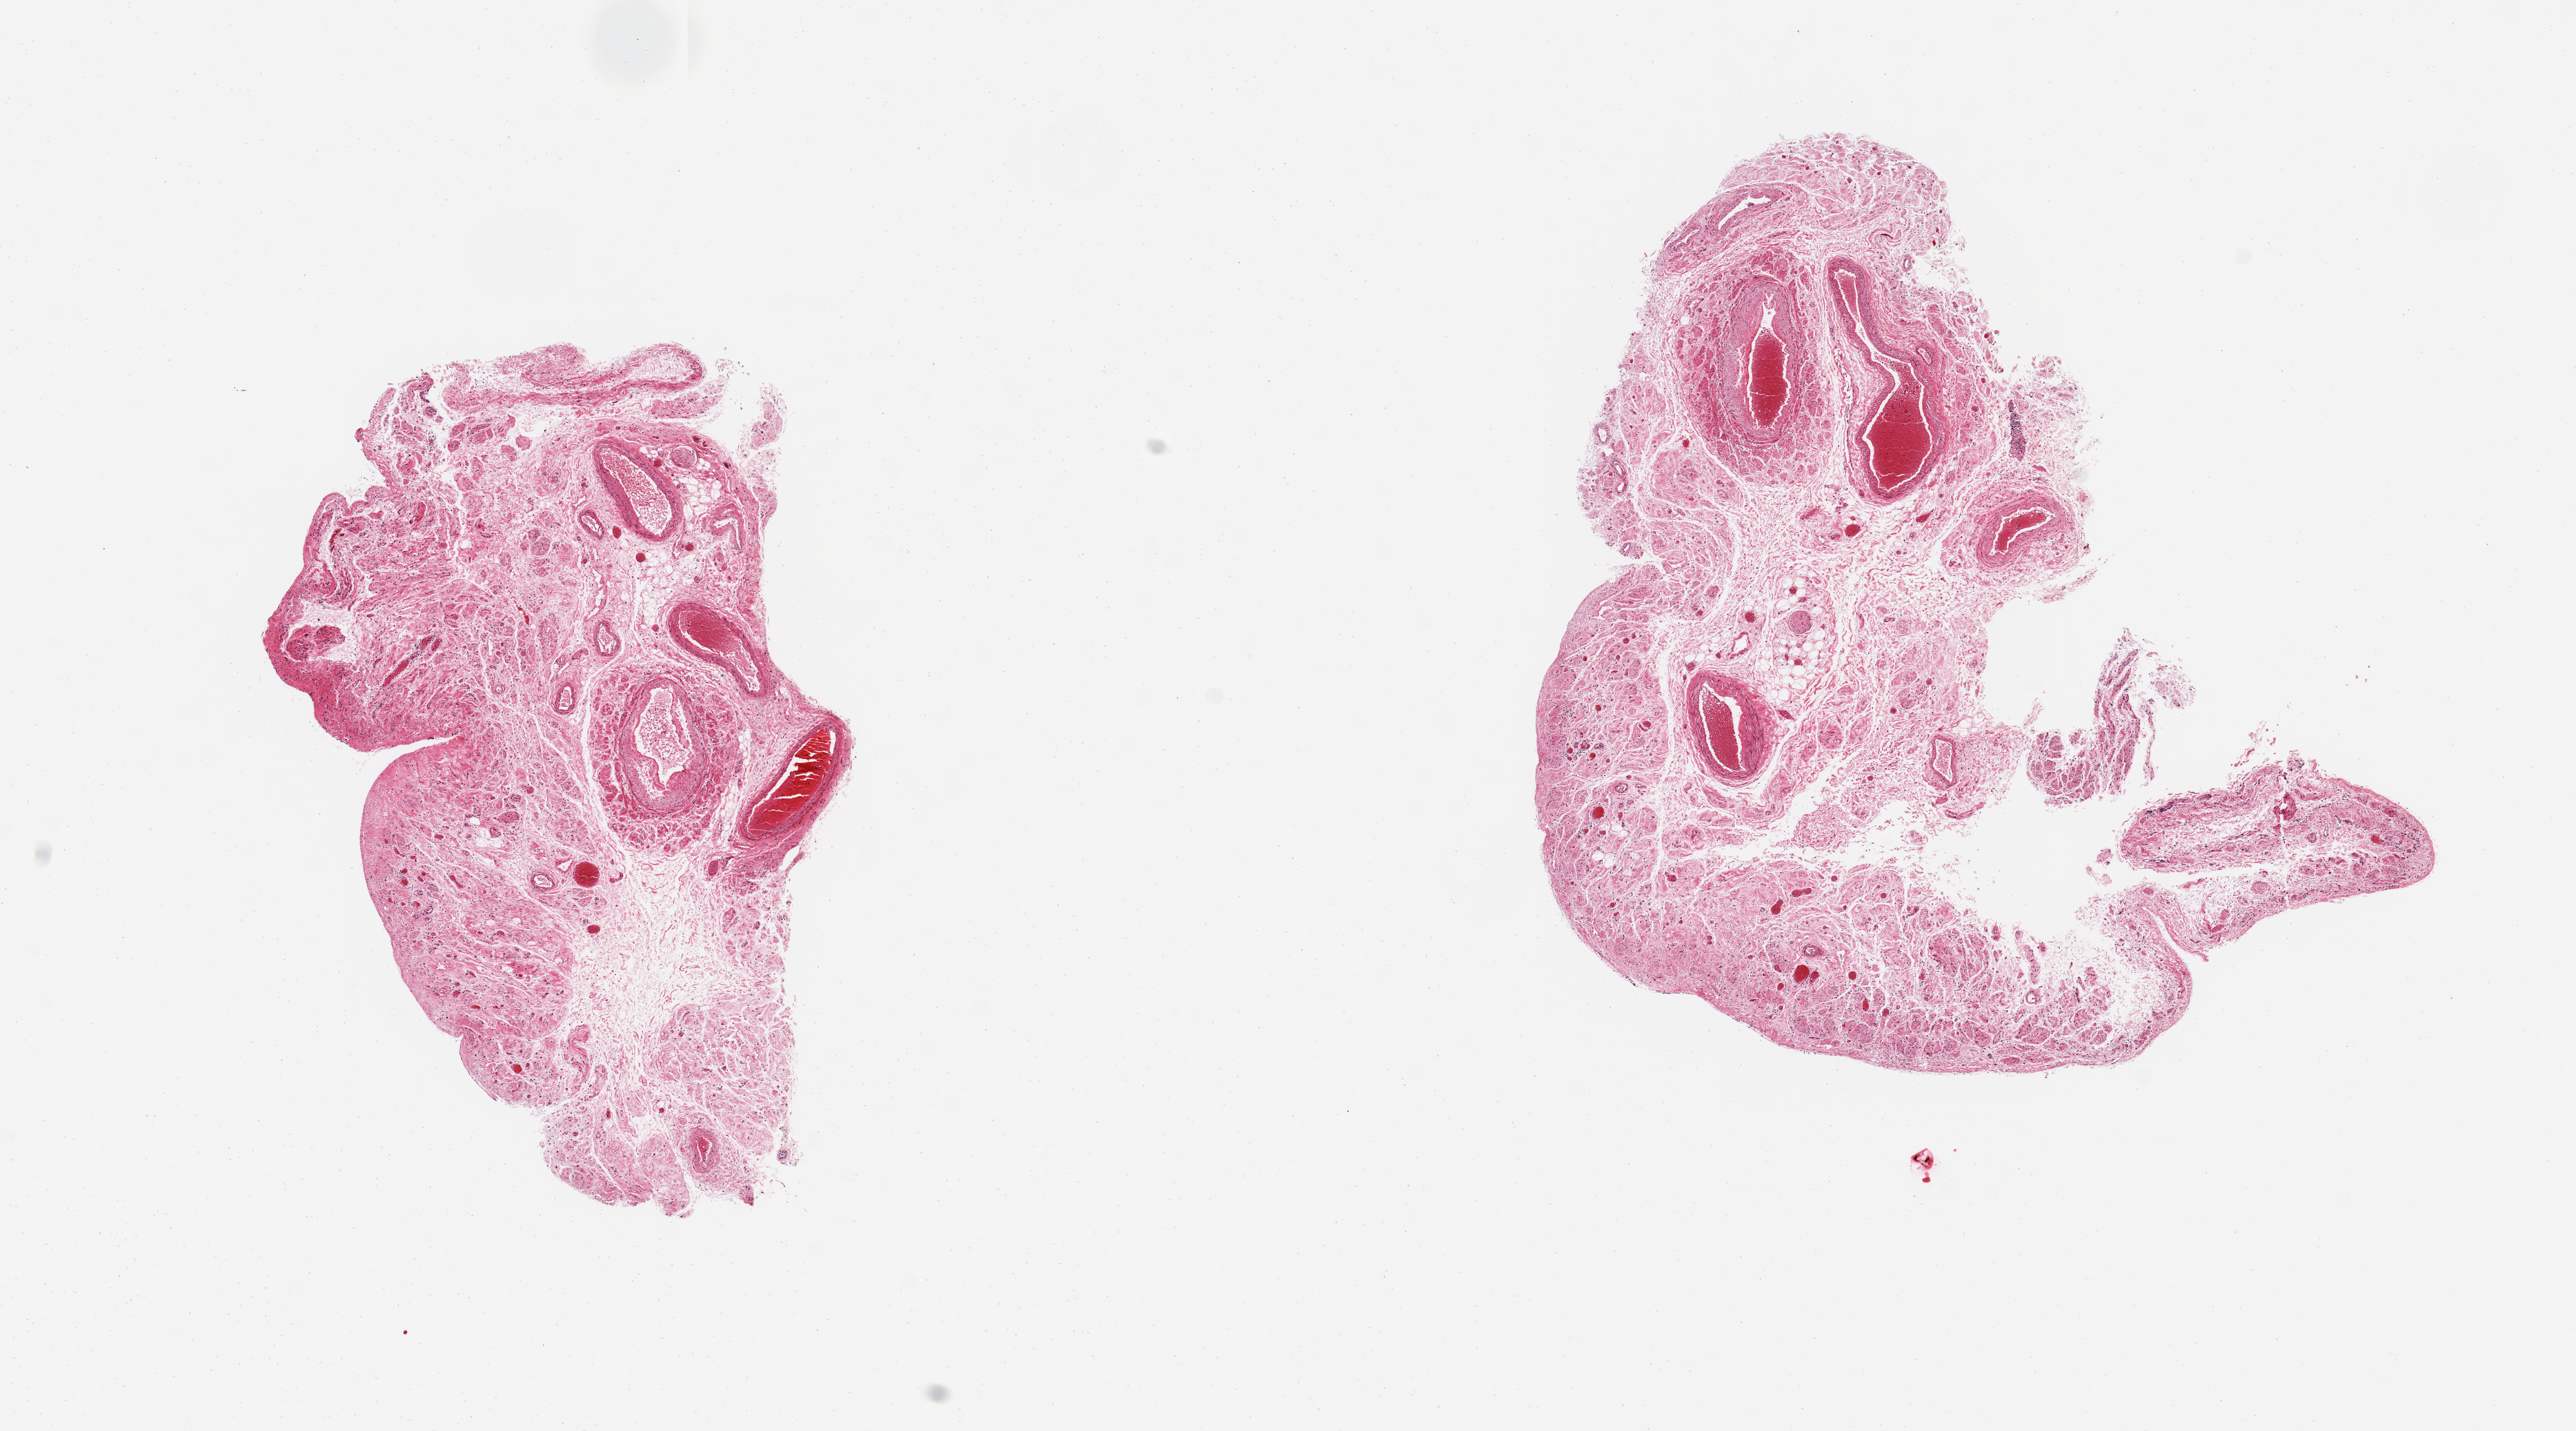
H&E whole-slide image, brightfield — low-resolution overview of the scanned area, about 14.8 x 8.2 mm. PAXgene-fixed, paraffin-embedded tissue. Target tissue: fallopian tube. Tissue donor sample. Female donor.
Pathologist's review note for this sample: 2 pieces fibrovascular tissue, no tube is present.